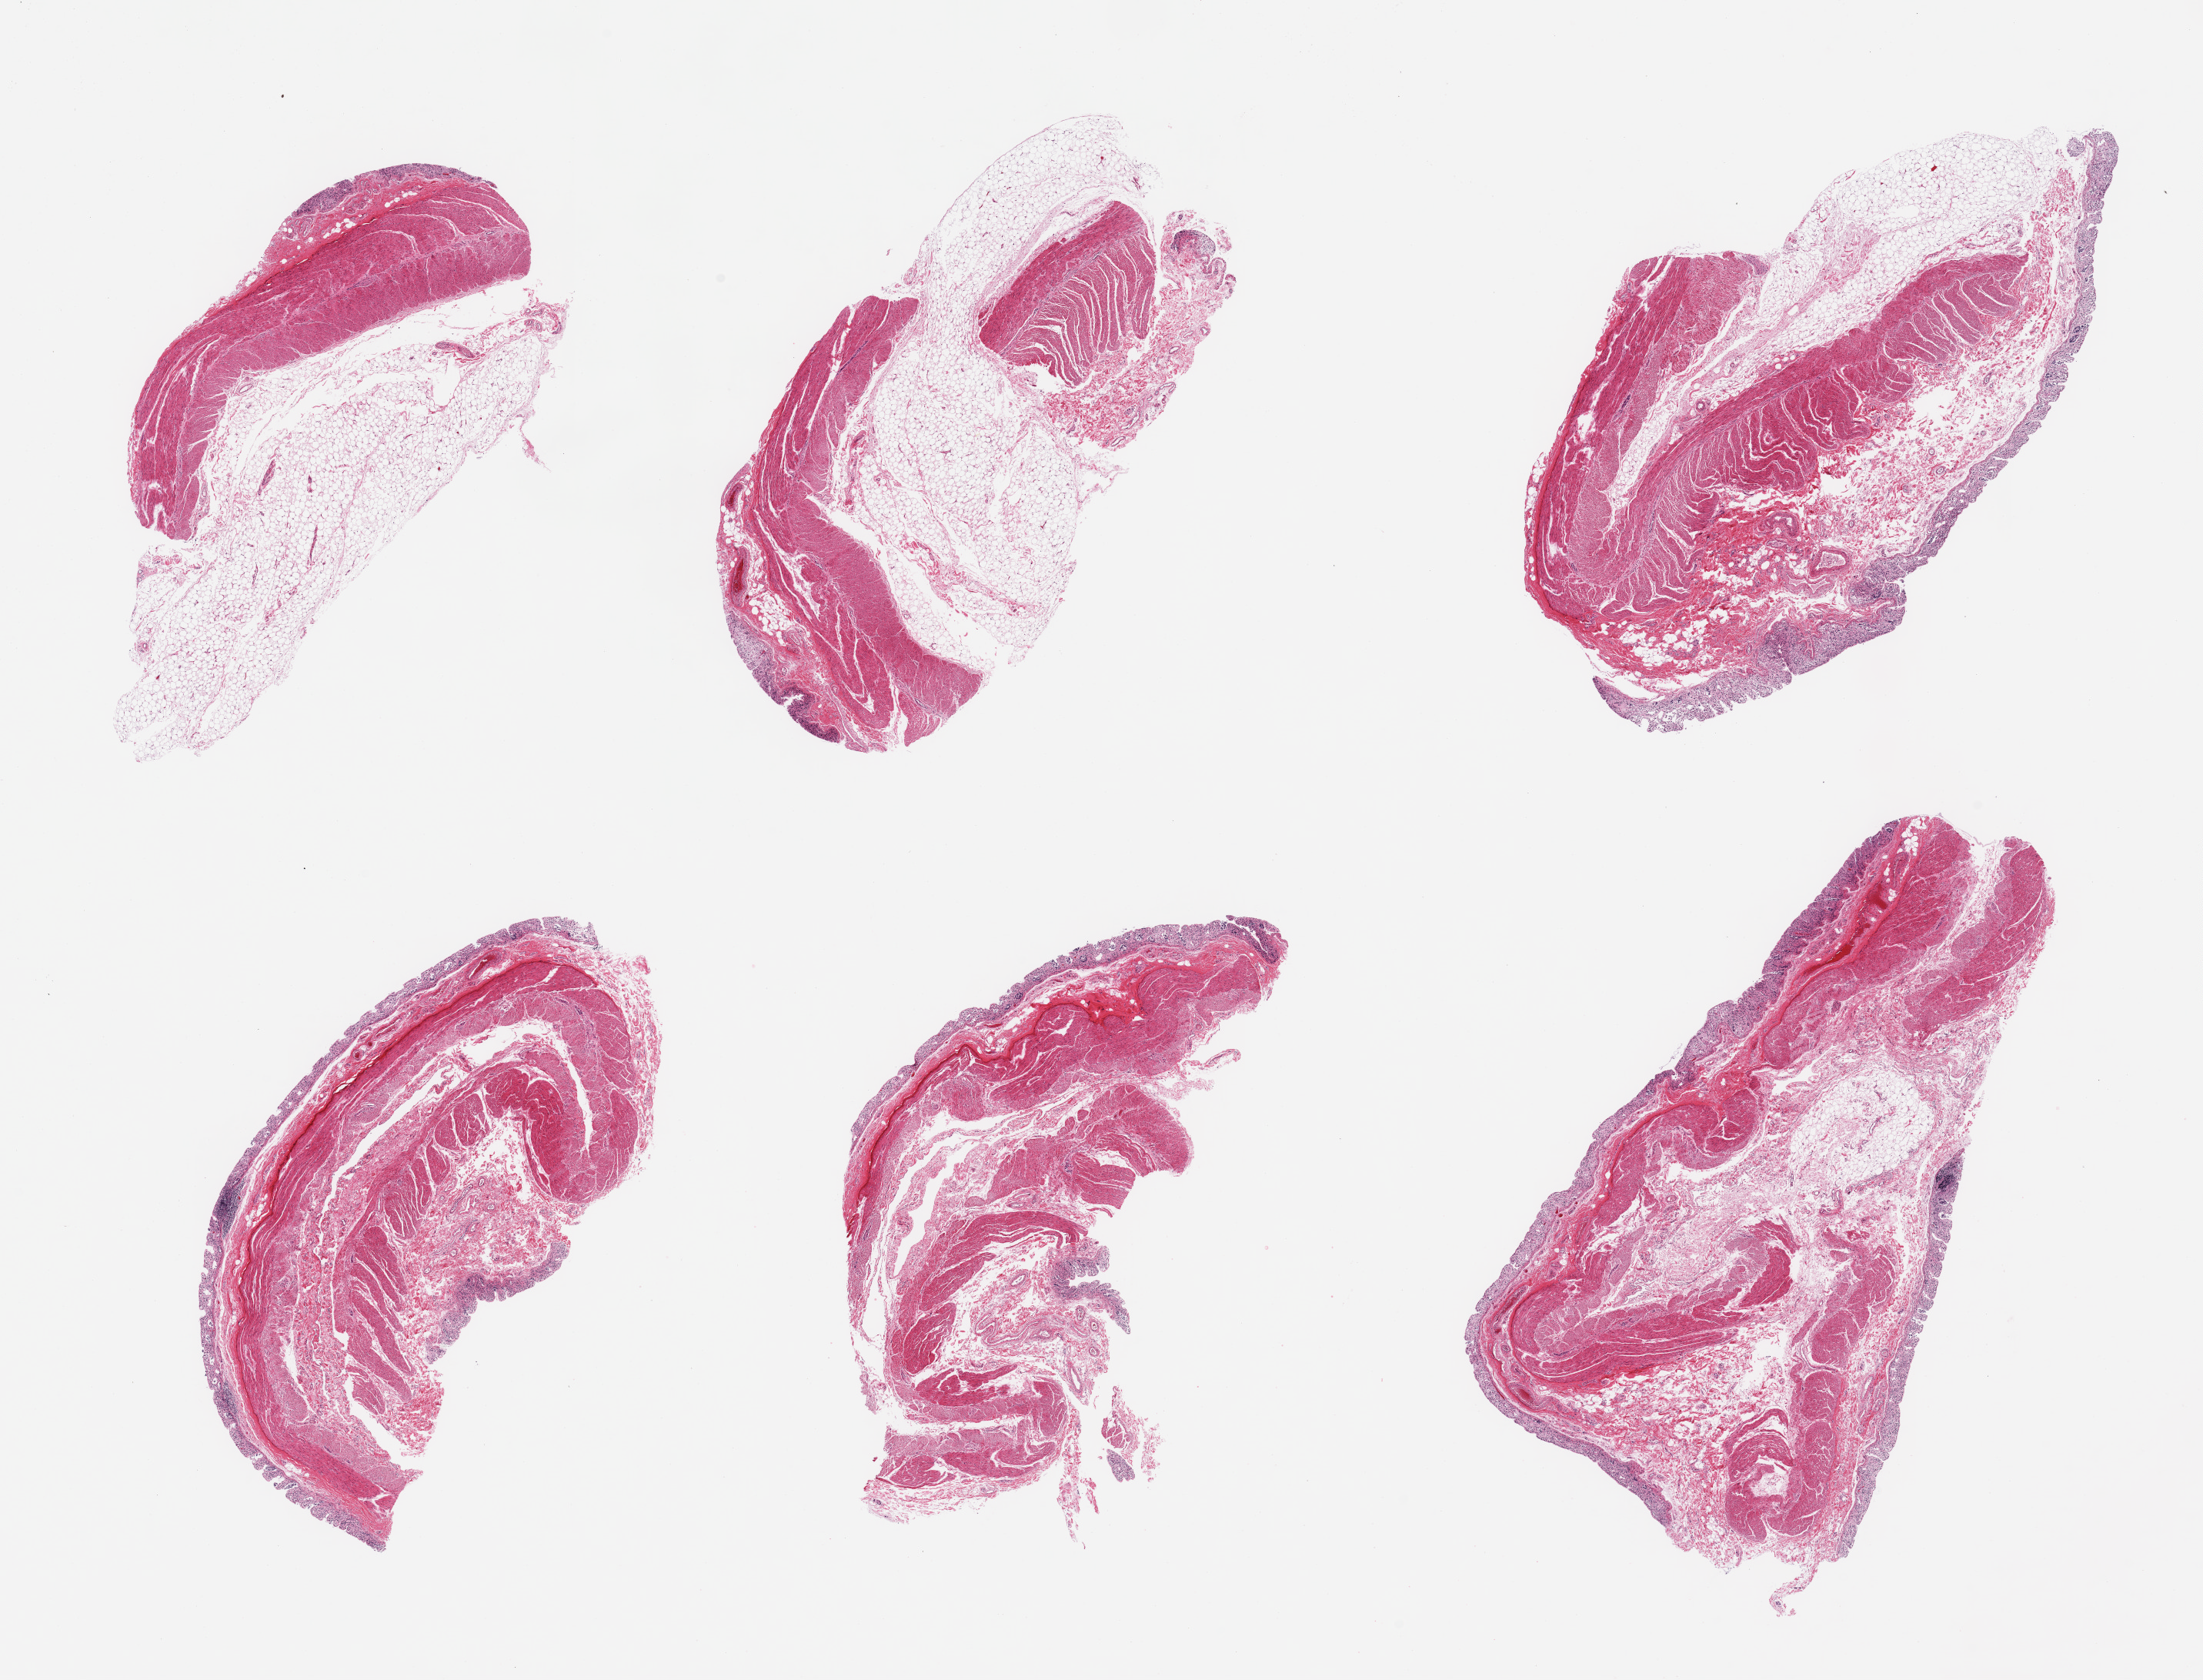
Digitized hematoxylin and eosin (H&E)-stained section, low-resolution overview of the scanned area, about 22.6 x 17.3 mm (from a 20x scan); PAXgene-fixed, paraffin-embedded tissue; target tissue: transverse colon; tissue donor sample. Female donor.
- reviewer comment on this tissue sample: 6 pieces; autolyzed mucosa, intact muscularis; abundant adventitial fat